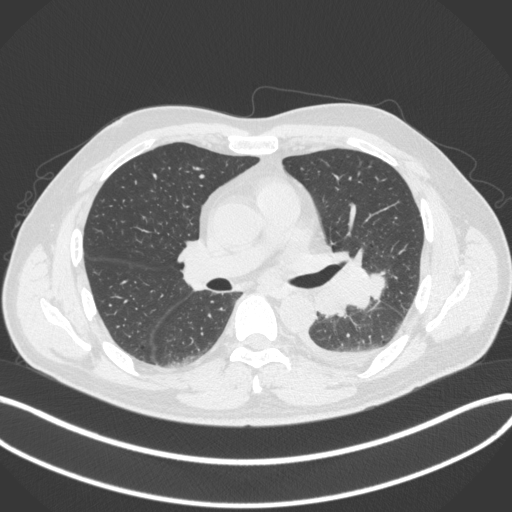
Chest CT, one axial slice; position 203 of 350 along the scan axis; reconstruction kernel B31f; lung window (W 1500 / L -600 HU); 512 × 512 image matrix. Male patient, age 58 years. Case-level facts recorded for this patient, not image findings: clinical TNM (as recorded): T3 N1 M1b; histopathological grade: G3.
Annotated regions visible in this slice (rectangle marked by the reading radiologist):
- lung tumour (recorded histology: small cell carcinoma): bounding box (x1, y1, x2, y2) in pixels: (318, 264, 389, 314)